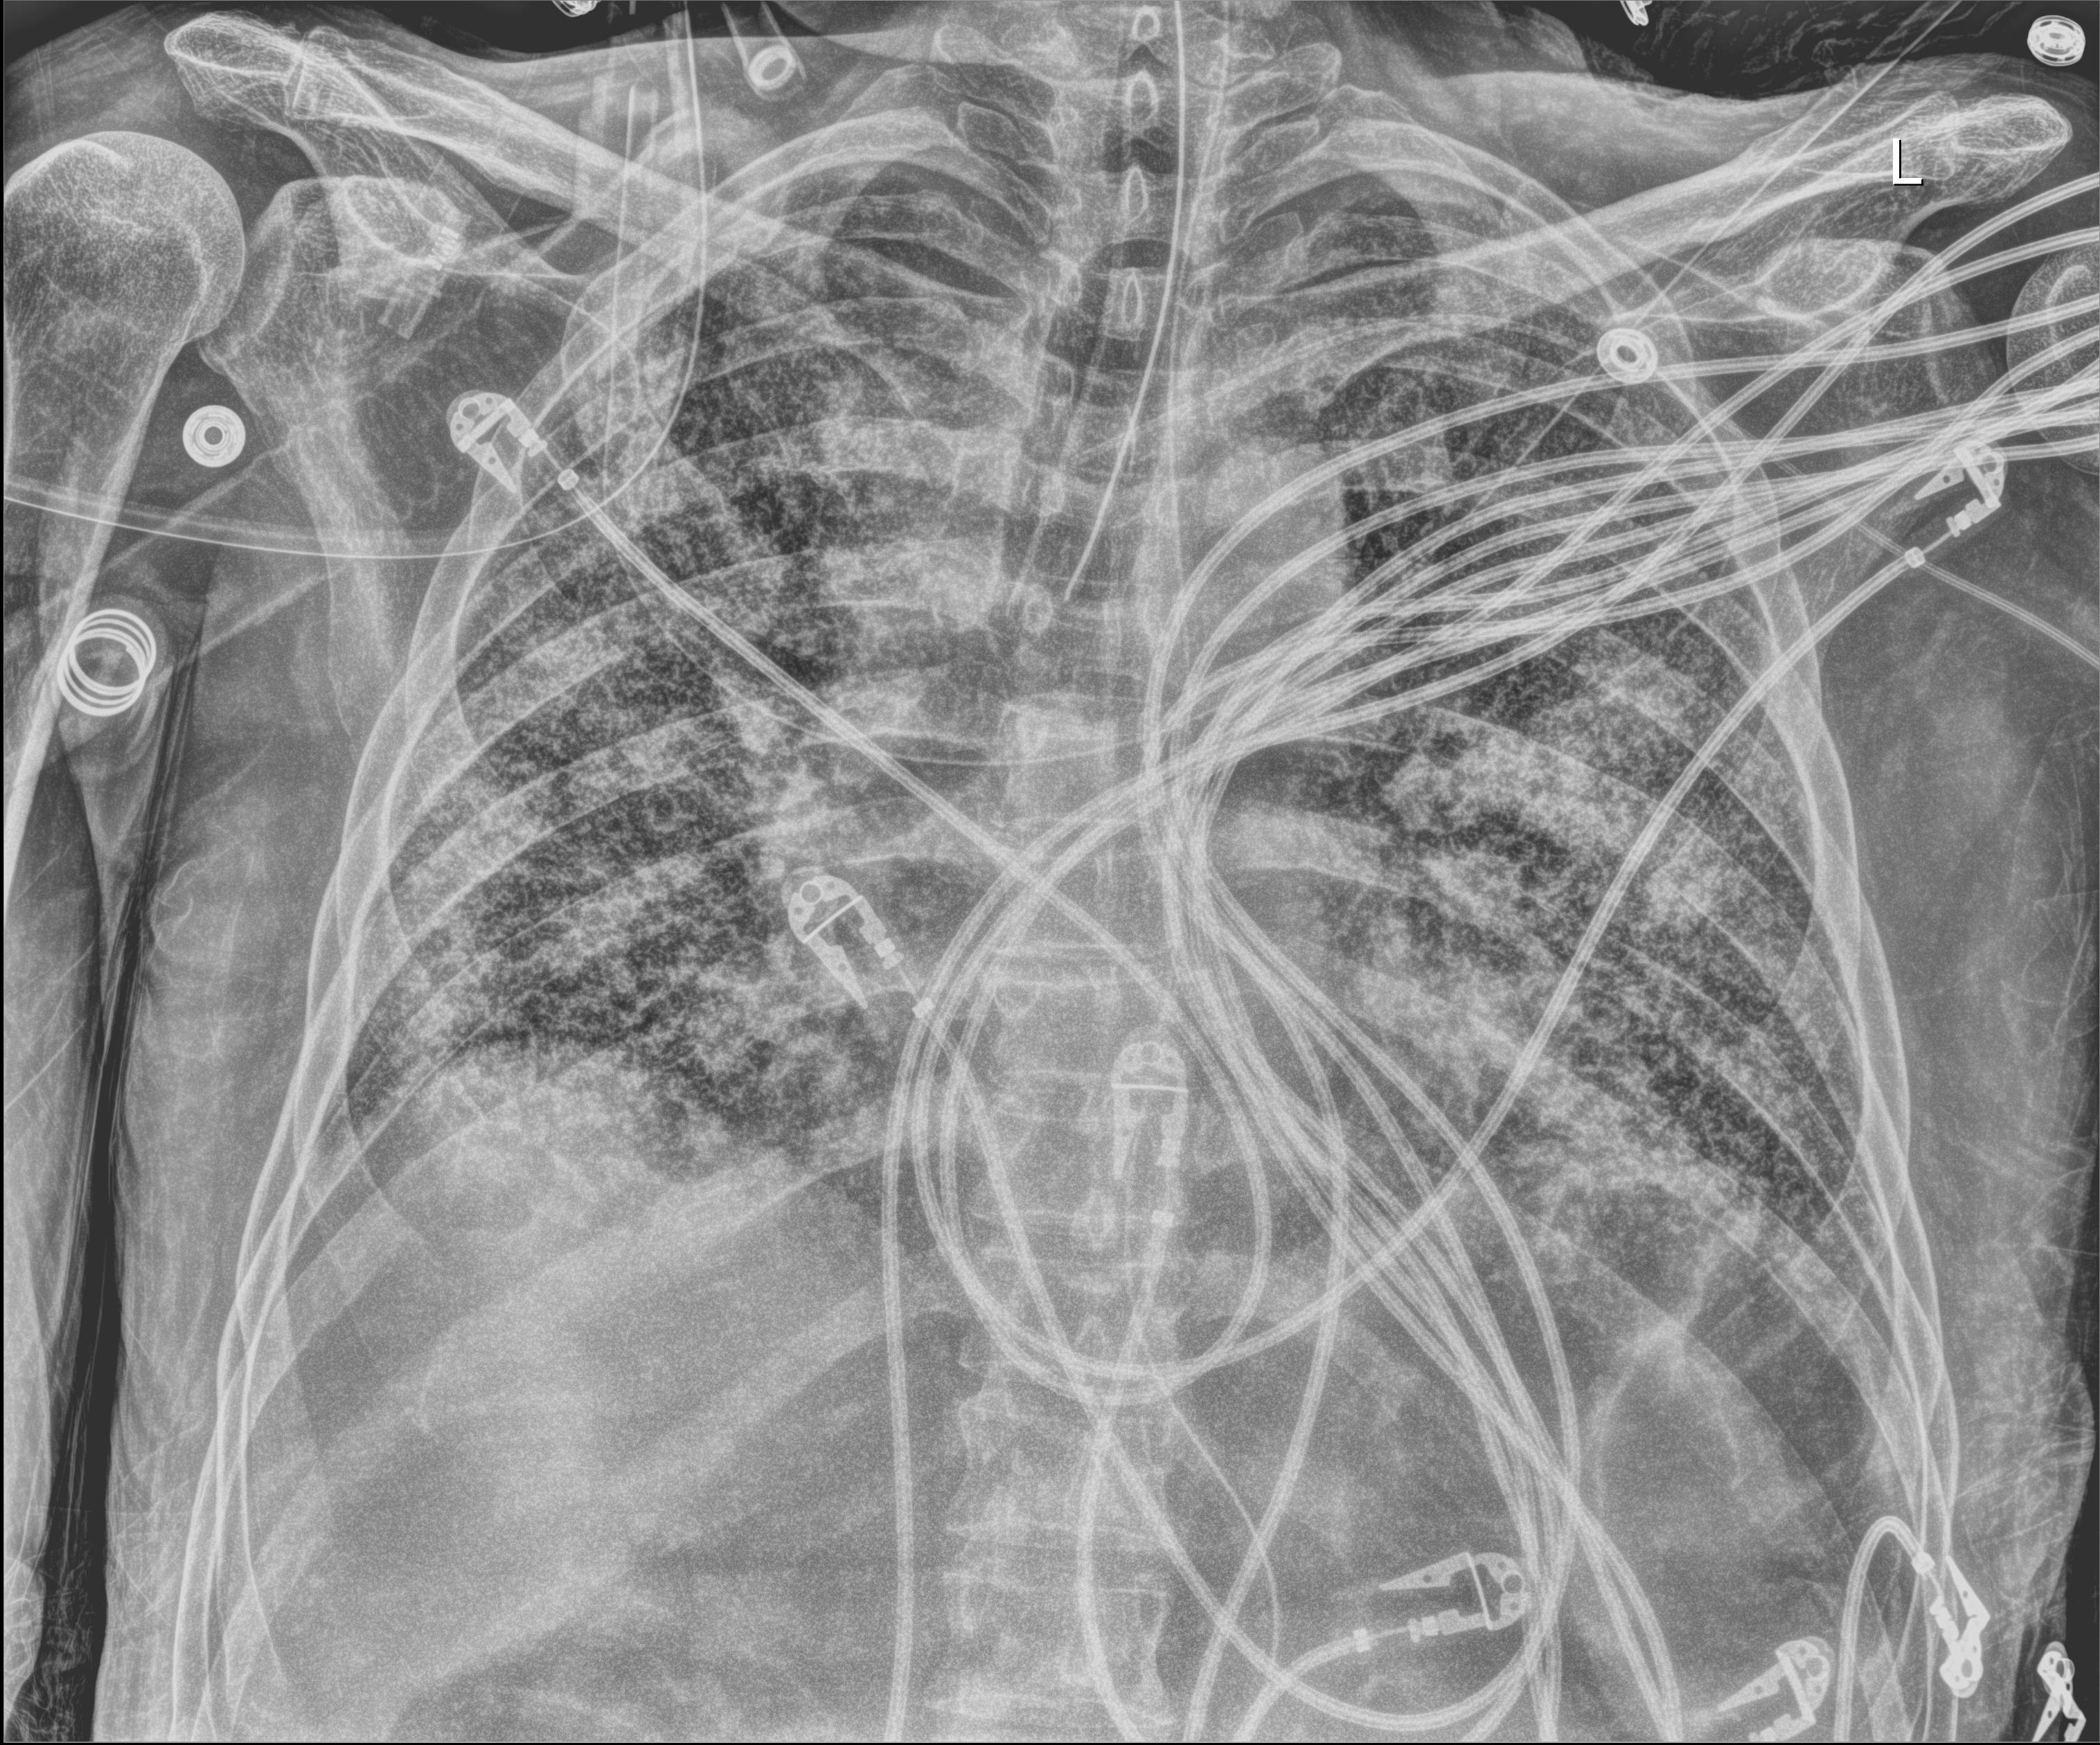
Portable chest radiograph, anteroposterior (AP) projection. Patient hospitalised with COVID-19; male, aged 60–74 years.
From the hospital-stay record, not from the radiograph (when in the stay this image was taken is not recorded): mechanically ventilated during this hospital stay: yes.